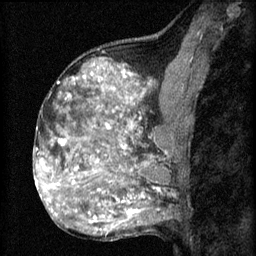
Breast MRI (dynamic contrast-enhanced), one sagittal slice; position 34 of 60 along the scan axis; 3 images stored at this slice position (order not interpretable as contrast timing); 1.5 T; TE 4.2 ms, TR 8.2 ms; 2 mm slice thickness; 256 × 256 image matrix, field of view 180 × 180 mm. Female patient, age 48 years.
Outlined on this slice (semi-automatic segmentation, software-assisted and operator-edited):
- analysis volume of interest (the breast-tissue region the enhancement analysis was run in; not a lesion): bounding box [x1, y1, x2, y2] px = [61, 138, 153, 201]
- tumour enhancement mask (voxels above the 70 % enhancement threshold inside the analysis volume of interest): [61, 140, 143, 201]